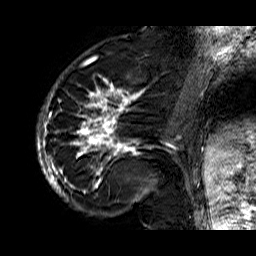
Breast MRI (dynamic contrast-enhanced), one sagittal slice; position 19 of 60 along the scan axis; dynamic contrast-enhanced series, time point 2 of 6 at this slice position (early post-contrast); 1.5 T; TE 6.3 ms, TR 32.9 ms; 256 × 256 image matrix. Female patient. Case-level facts recorded for this patient, not image findings: setting: breast cancer imaged before/during neoadjuvant chemotherapy; receptor status: HR-positive, HER2-negative.
Outlined on this slice (semi-automatic segmentation, software-assisted and operator-edited):
- analysis volume of interest (the breast-tissue region the enhancement analysis was run in; not a lesion): bounding box (x1, y1, x2, y2) in pixels: (36, 74, 176, 210)
- tumour enhancement mask (voxels above the 100 % enhancement threshold inside the analysis volume of interest): (36, 75, 176, 205)